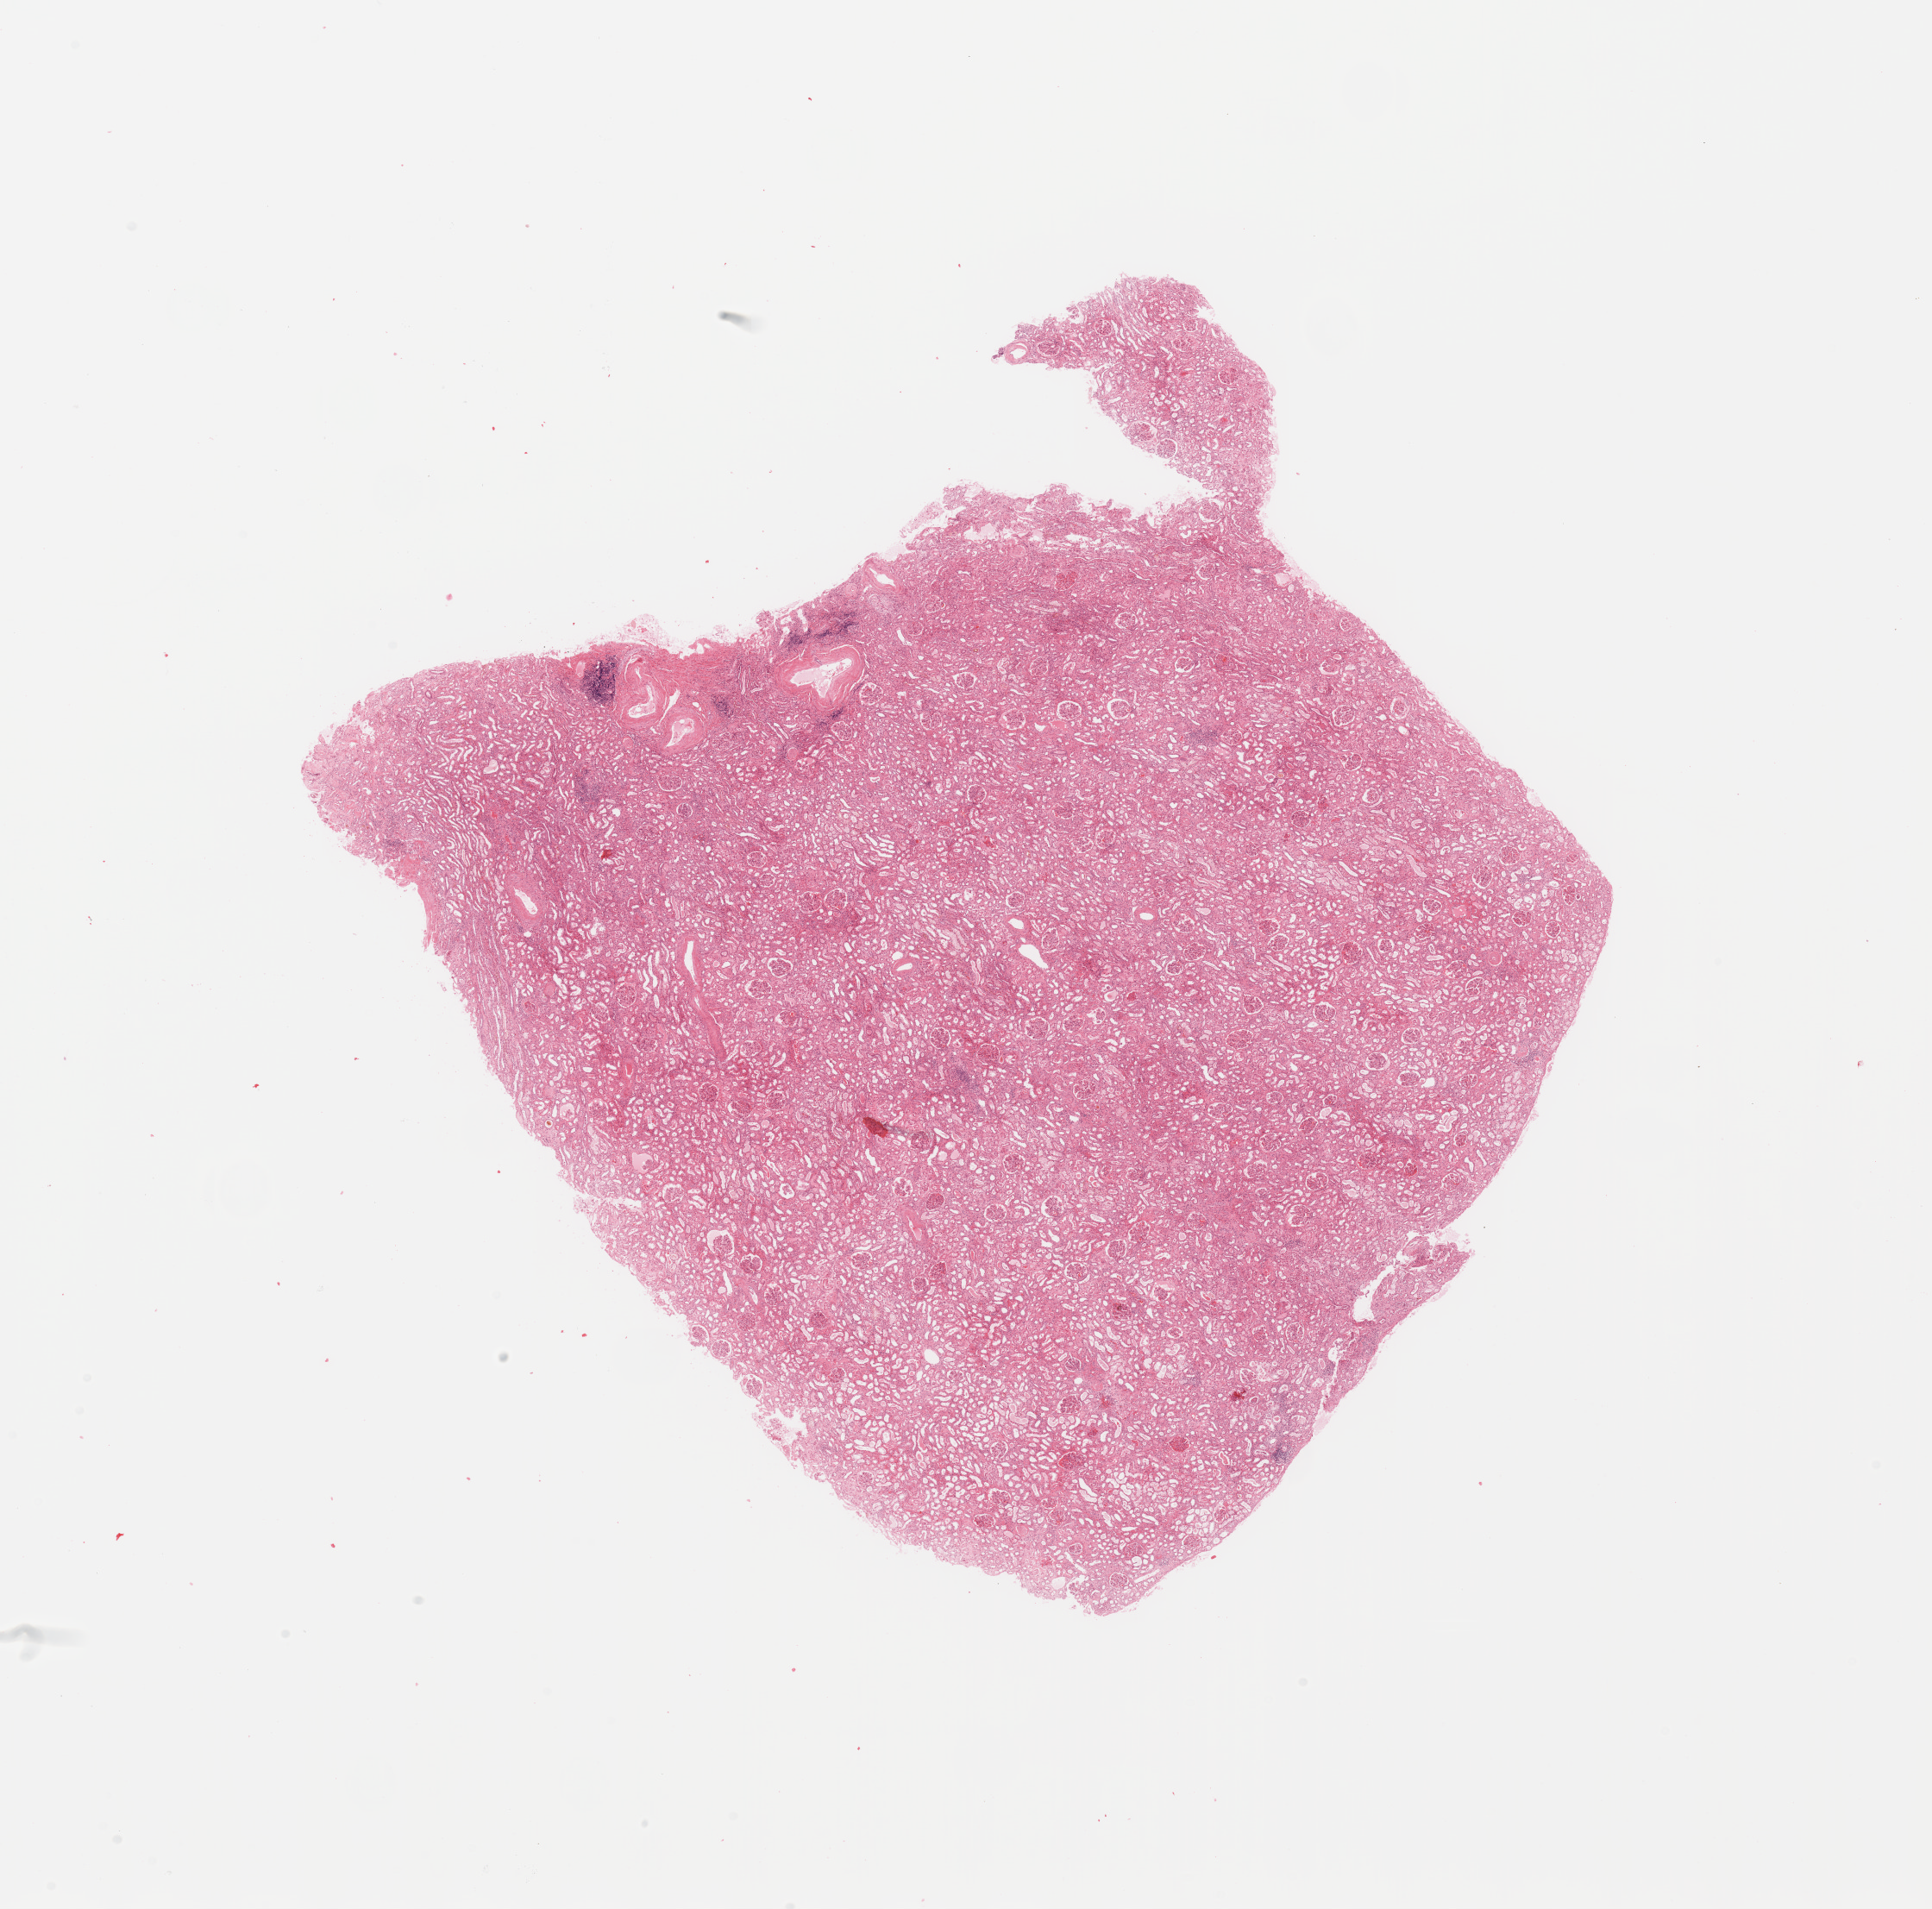
Hematoxylin and eosin (H&E) stained whole-slide image — whole scanned area (about 17.7 x 17.5 mm, acquisition: 20x scan) shown as a low-resolution overview; normal (non-tumour) tissue sample, sampled site: kidney. Female, 68 y/o.
• this section: normal (non-tumour) tissue from the same patient
• patient diagnosis: Renal cell carcinoma, NOS